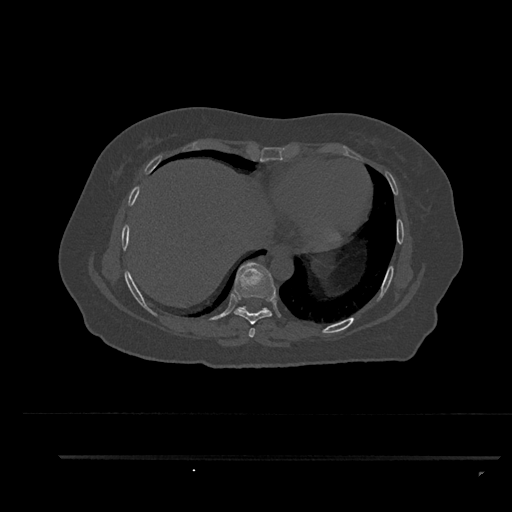
CT including the spine, one axial slice; slice 451 of 797 in the series (ordered by position); reconstruction kernel Br40s/3; 120 kVp; bone window (W 1800 / L 400 HU); 0.5 mm slice thickness; 512 × 512 image matrix, field of view 408 × 408 mm. Patient: female, 44 years. From the clinical record (not read from this slice): primary cancer: renal; vertebrae with lytic lesions (as recorded): L1.
Outlined on this slice (semi-automatic segmentation, software-assisted and operator-edited):
- T7 vertebra: bounding box [x1, y1, x2, y2] px = [249, 328, 255, 338]
- T8 vertebra: [234, 262, 276, 325]
- T9 vertebra: [235, 306, 269, 313]